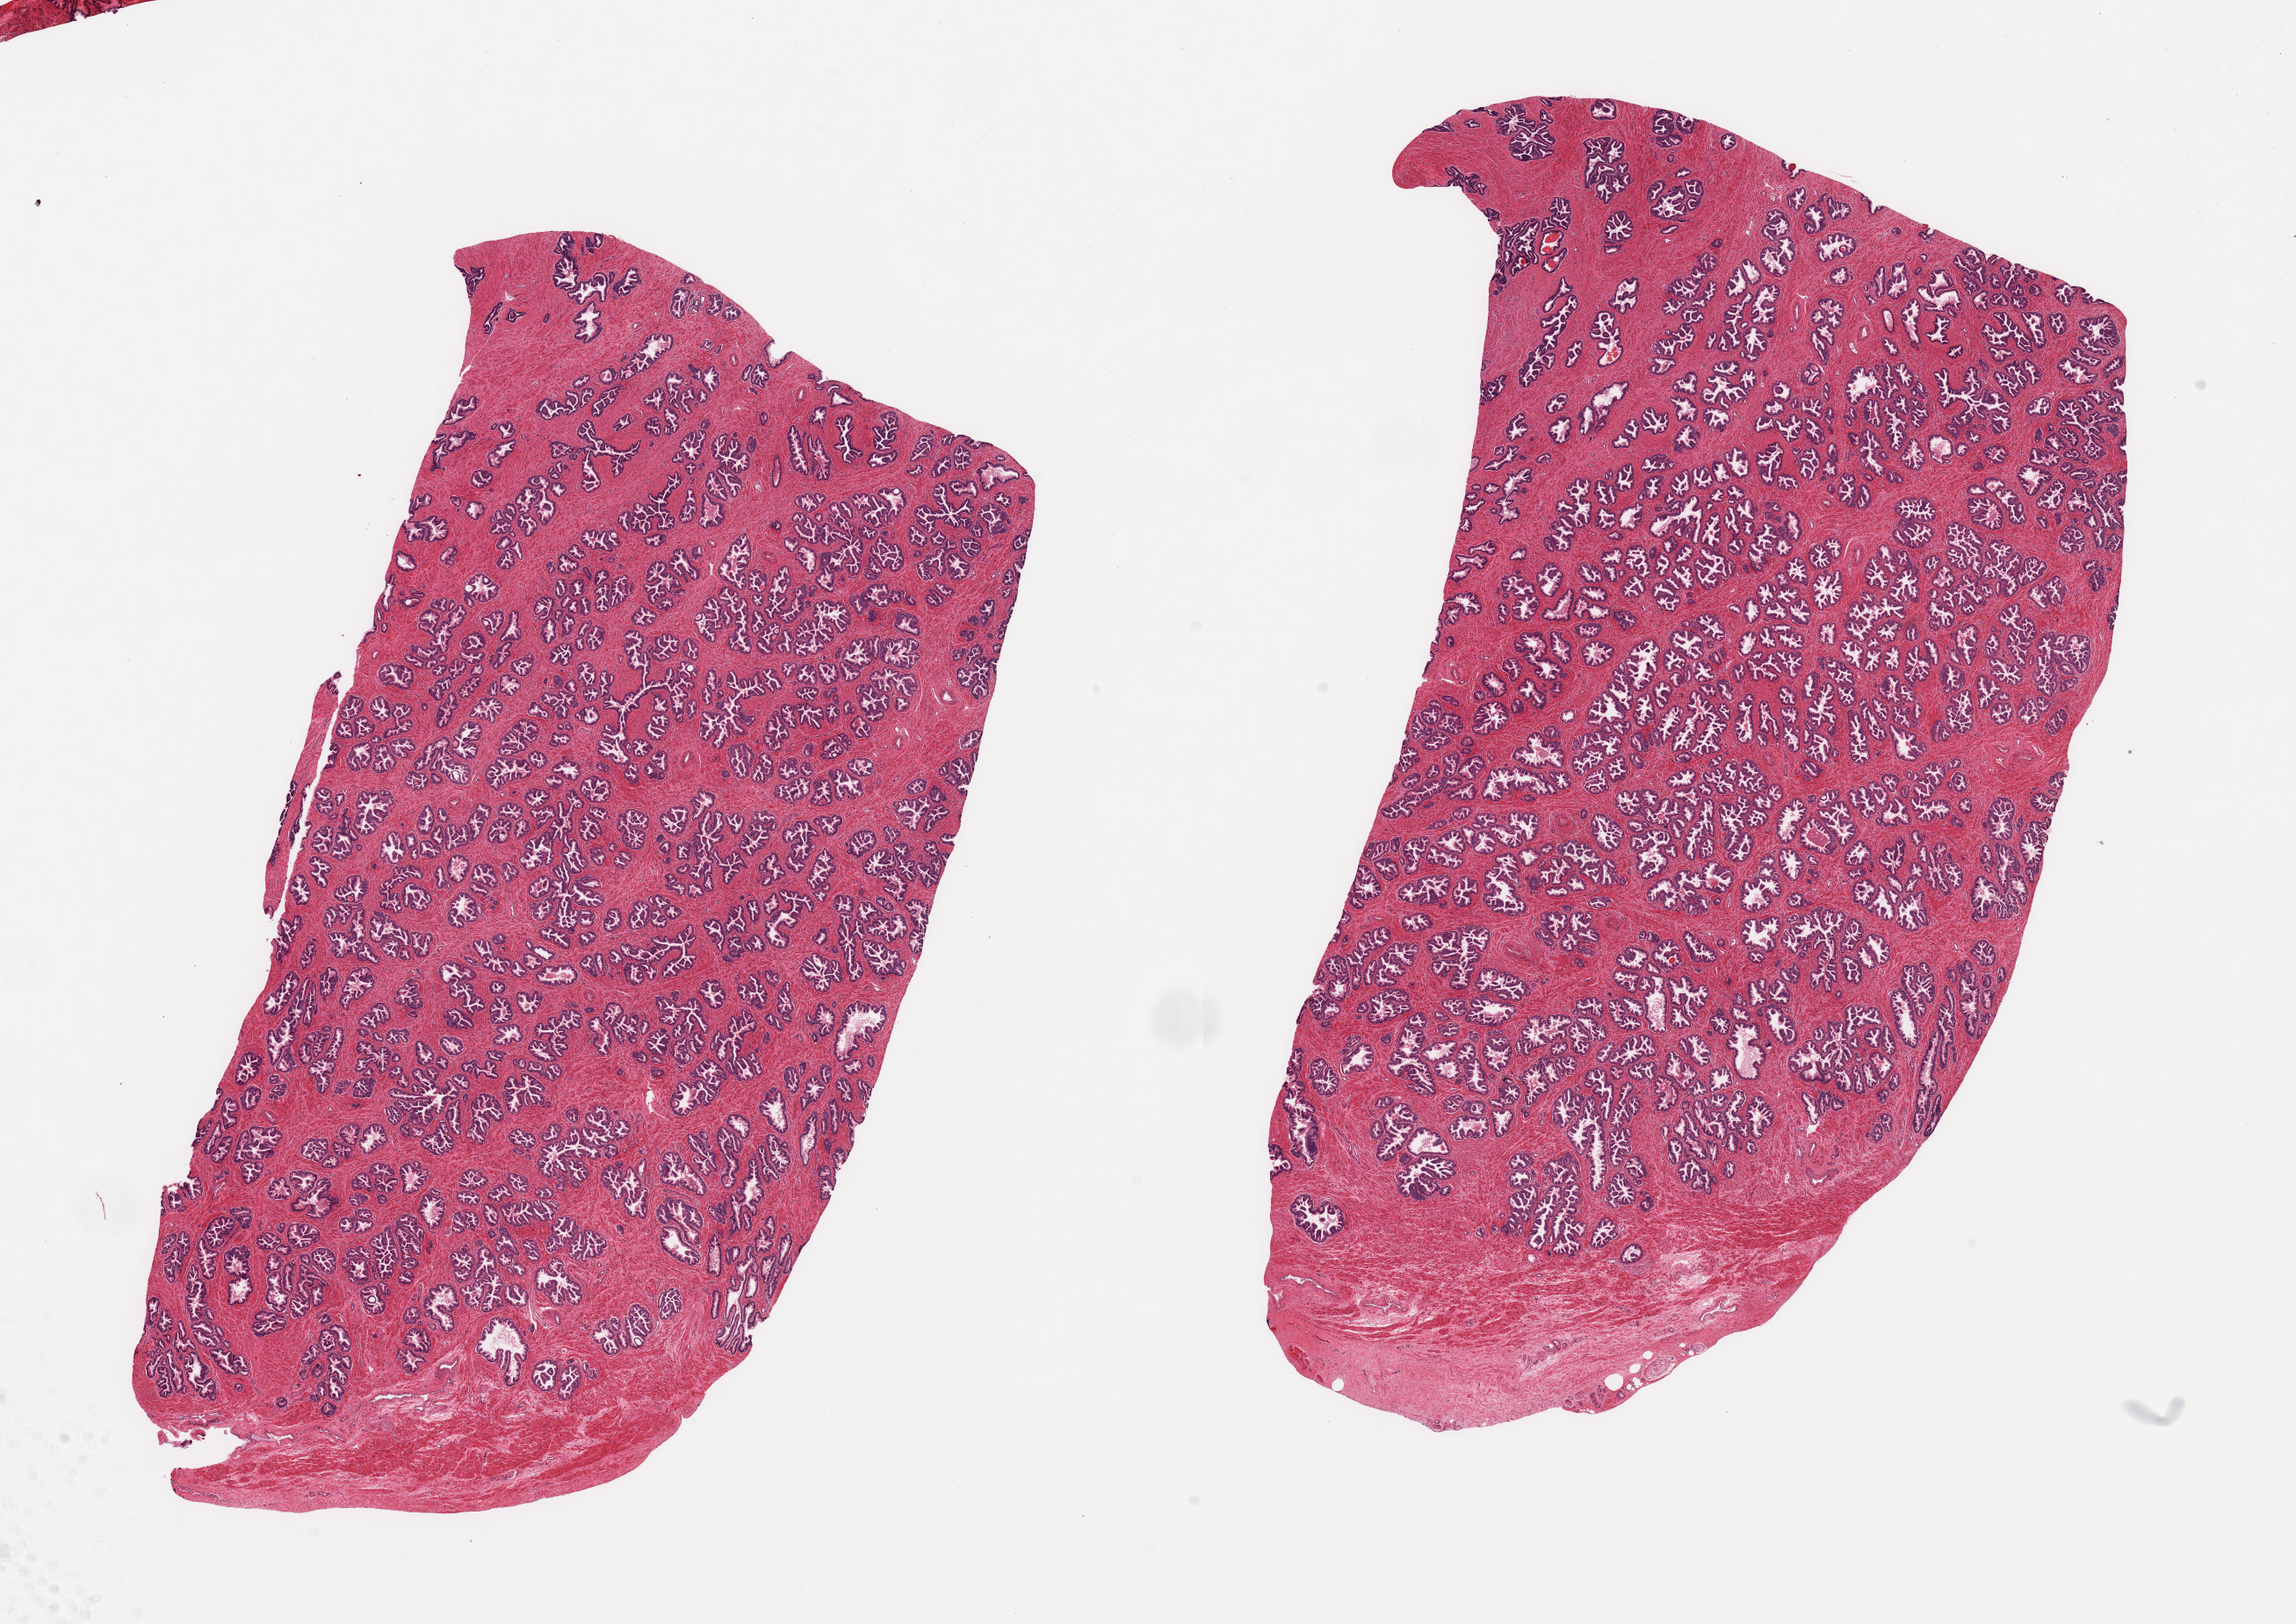
Digitized hematoxylin and eosin (H&E)-stained section, a low-resolution overview of the entire scanned area, about 20.7 x 14.6 mm (slide scanned at 20x). PAXgene-fixed, paraffin-embedded tissue. Target tissue: prostate. Donor tissue sample. Male donor.
Review note (as recorded): 2 pieces, abundant well-preserved glands.